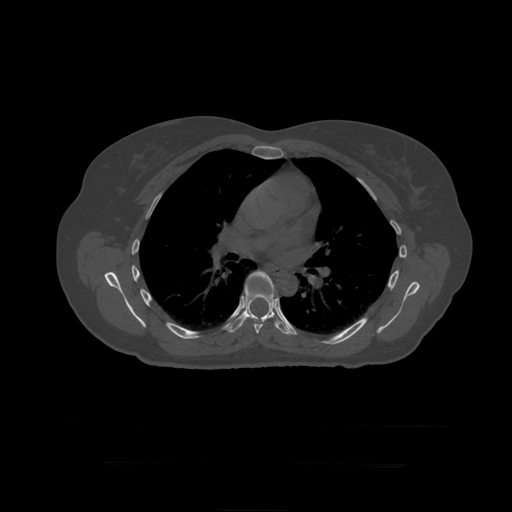
CT including the spine, one axial slice. Position 291 of 399 along the scan axis. Reconstruction kernel STANDARD. Bone window (W 1800 / L 400 HU). 1.25 mm slice thickness. 512 × 512 image matrix. Patient age 41 years. From the clinical record (not read from this slice): primary cancer: breast.
Structures marked on this image (semi-automatic segmentation, software-assisted and operator-edited):
- T7 vertebra: bounding box <244,271,275,334> (left, top, right, bottom; pixels)
- T8 vertebra: <227,284,290,335>